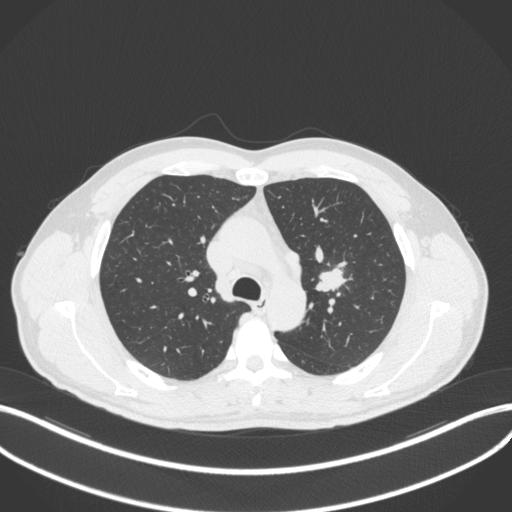
Chest CT, one axial slice. Position 296 of 383 along the scan axis. Reconstruction kernel B31f. 120 kVp. Lung window (W 1500 / L -600 HU). 512 × 512 image matrix. Patient: male, 50 years. Case-level facts recorded for this patient, not image findings: clinical TNM (as recorded): T1c N1 M1b.
Annotated regions visible in this slice (rectangle marked by the reading radiologist):
- lung tumour (recorded histology: squamous cell carcinoma): box from (x=315, y=261) to (x=349, y=293) px